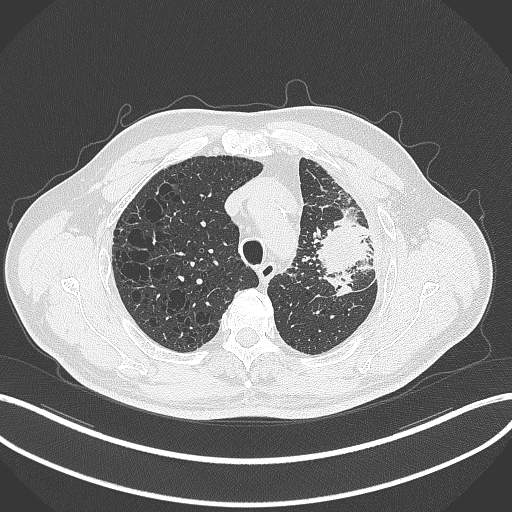
Chest CT, one axial slice. Position 250 of 297 along the scan axis. Reconstruction kernel B70f. Lung window (W 1500 / L -600 HU). 1 mm slice thickness. 512 × 512 image matrix, field of view 400 × 400 mm. Male patient, age 68 years. From the clinical record (not read from this slice): clinical TNM (as recorded): T3 N3 M1.
Structures marked on this image (rectangle marked by the reading radiologist):
- lung tumour (recorded histology: adenocarcinoma): bounding box [x1, y1, x2, y2] px = [316, 202, 371, 285]